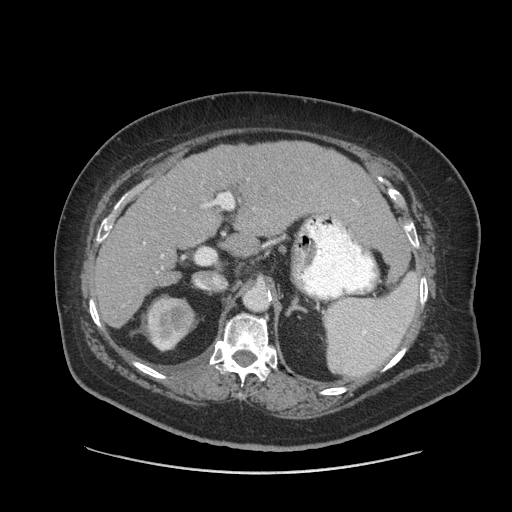
Contrast-enhanced abdominal CT (liver protocol), one axial slice; slice 49 of 91 in the series (ordered by position); reconstruction kernel STANDARD; 140 kVp; soft-tissue window (W 400 / L 40 HU); 2.5 mm slice thickness; 512 × 512 image matrix, field of view 420 × 420 mm. Case-level facts recorded for this patient, not image findings: diagnosis: hepatocellular carcinoma (patient treated with transarterial chemoembolisation; whether this scan precedes or follows treatment is not stated here); TNM stage (as recorded): Stage-I; Child-Pugh class: A; tumour differentiation: well differentiated.
Outlined on this slice (semi-automatically segmented with operator editing):
- liver parenchyma outside the tumour (the mass and vessels are separate outlines, so this box may not span the whole liver): bounding box <94,142,392,328> (left, top, right, bottom; pixels)
- liver vessels: <144,202,215,257>